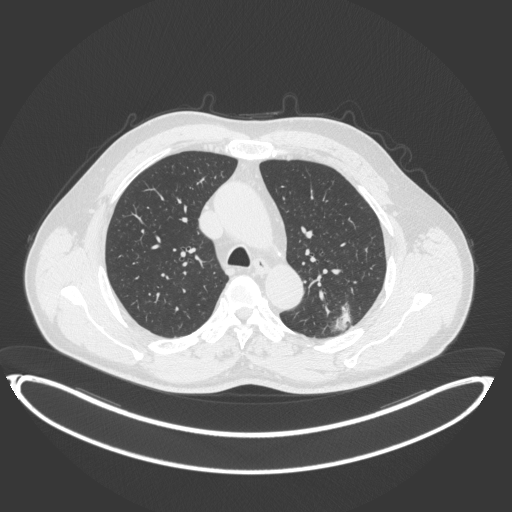
Chest CT, one axial slice. Slice 253 of 399 in the series (ordered by position). 120 kVp. Lung window (W 1500 / L -600 HU). 1 mm slice thickness. 512 × 512 image matrix. Patient: male, 58 years. From the clinical record (not read from this slice): clinical TNM (as recorded): T1c N0 M0; histopathological grade: G1-2.
Outlined on this slice (bounding box drawn by a radiologist):
- lung tumour (recorded histology: adenocarcinoma): bounding box [x1, y1, x2, y2] px = [327, 296, 358, 338]